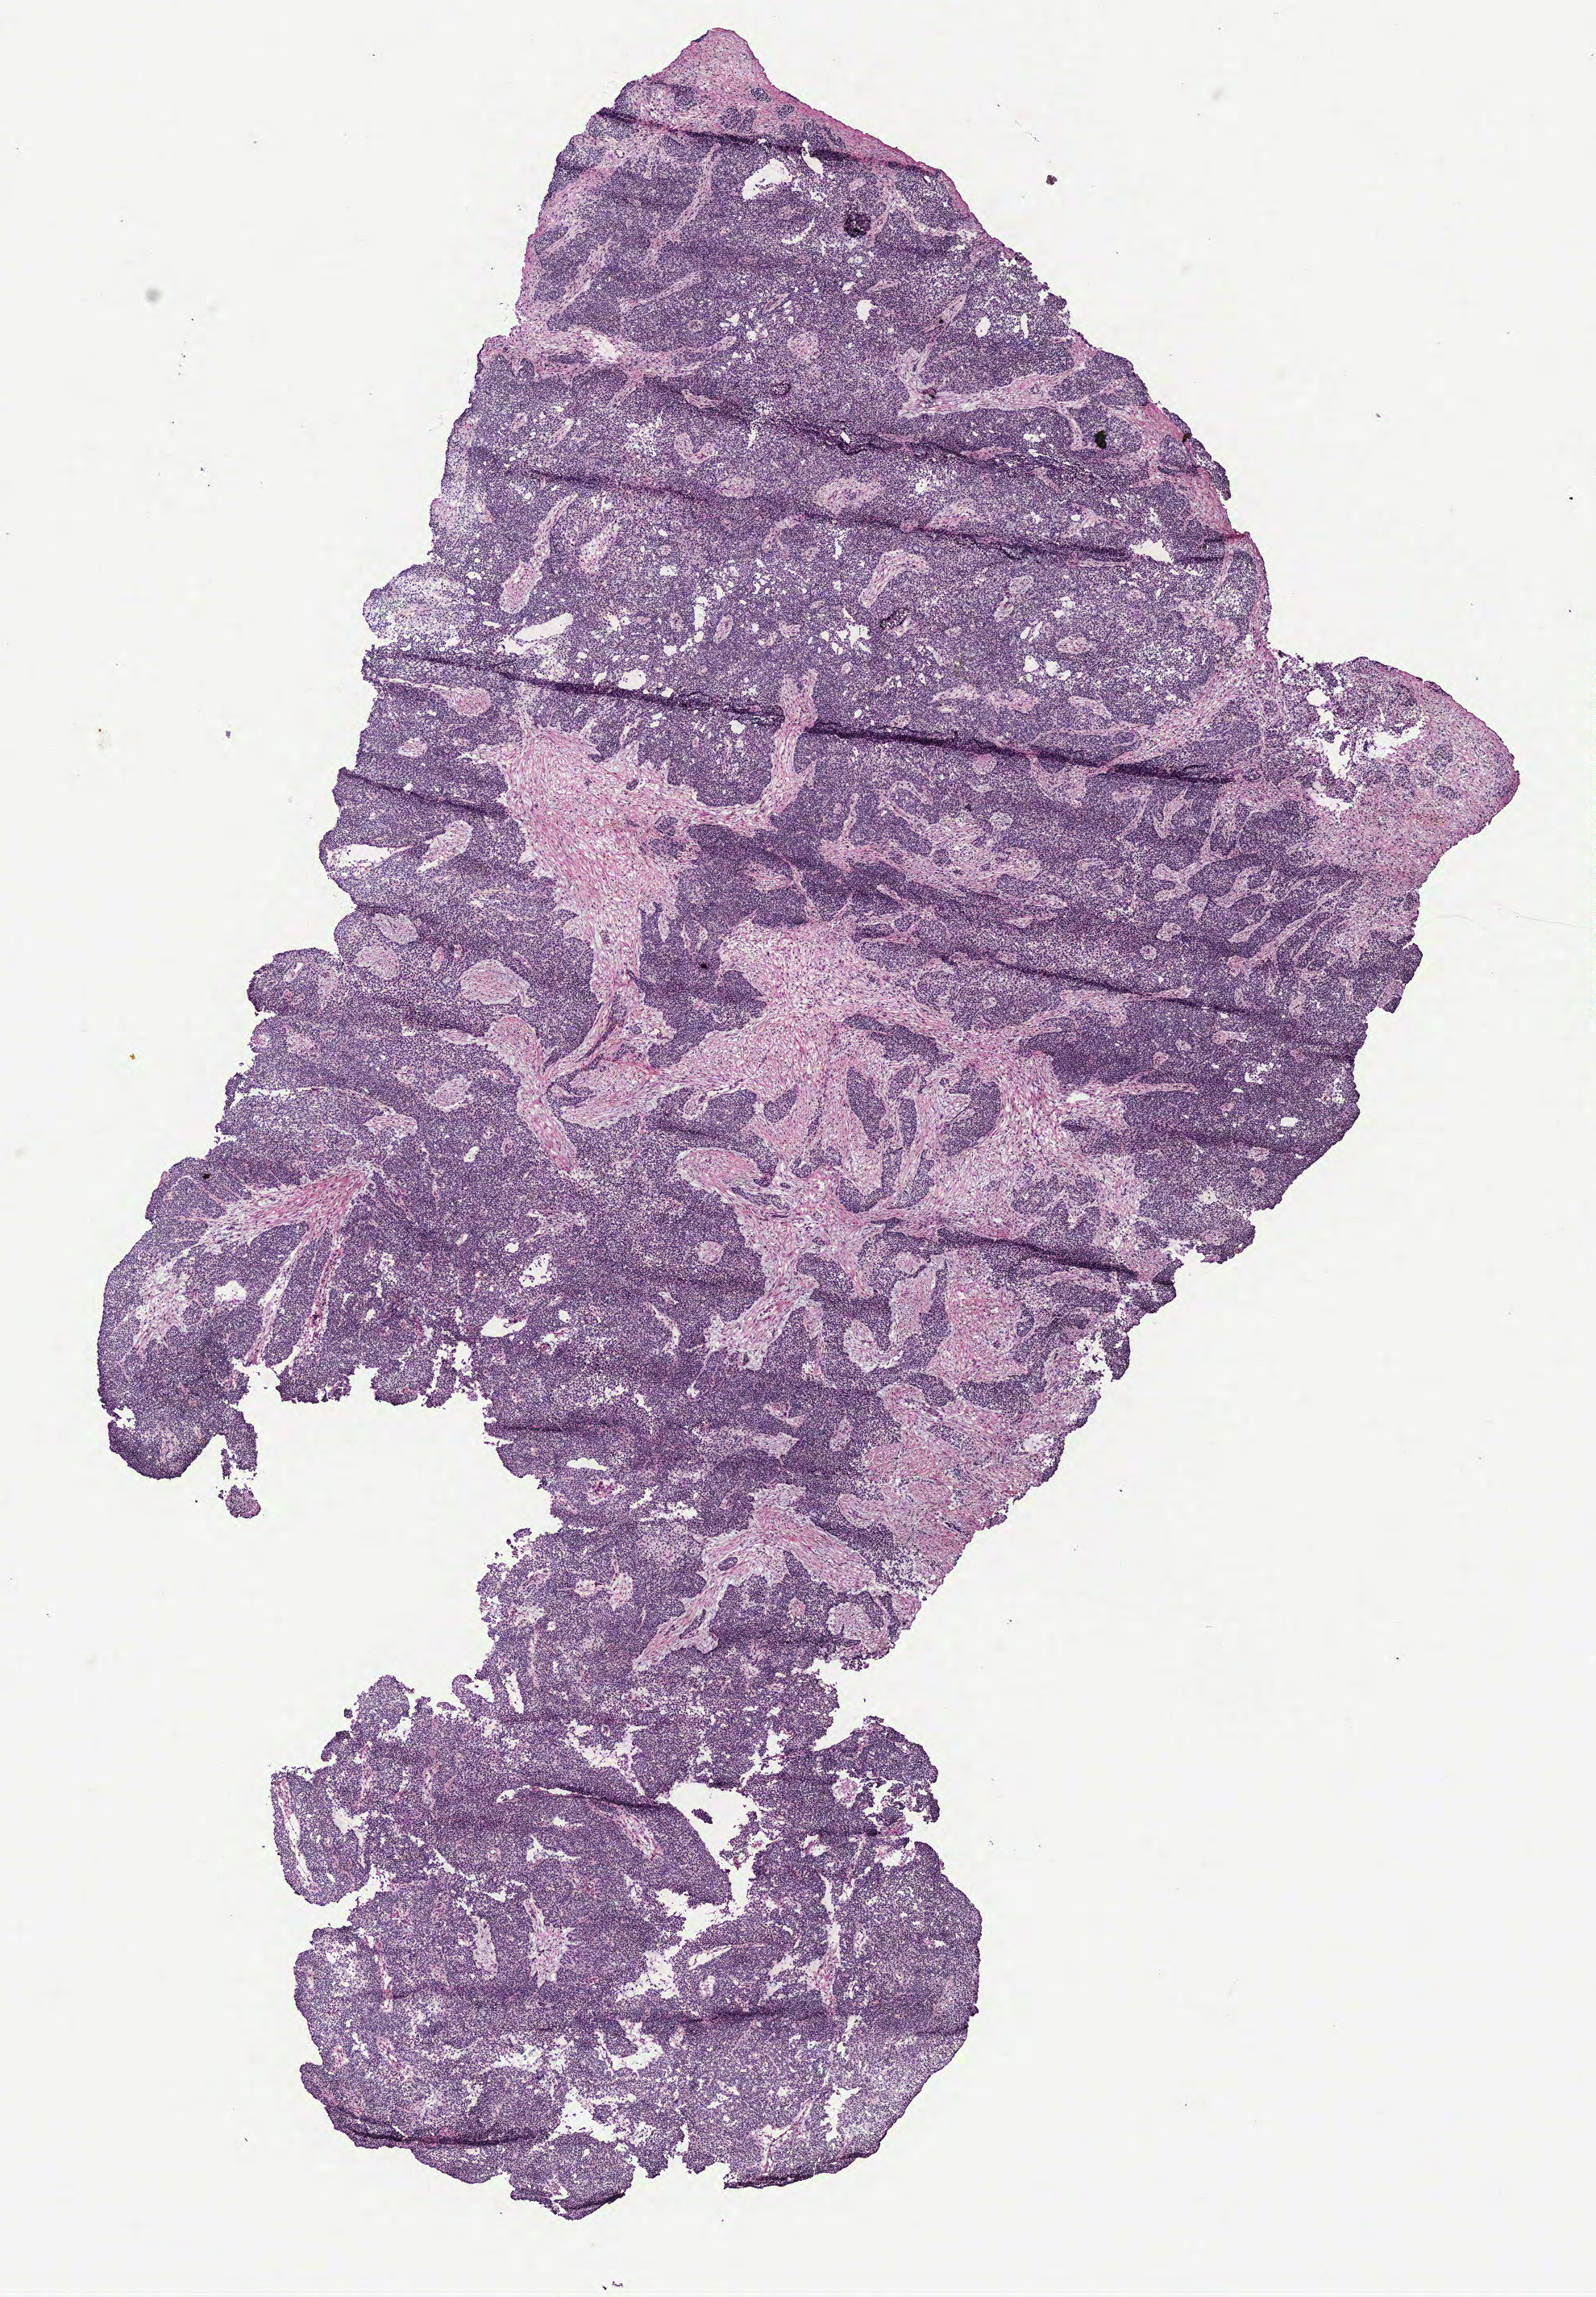
Whole-slide histology image, Hematoxylin and eosin (H&E) stained, whole scanned area (about 7.9 x 11.4 mm) shown as a low-resolution overview. Tumour tissue sample, ovary. 48-year-old female patient.
• primary tumour site (as recorded): ovary
• histologic diagnosis: Serous adenocarcinoma, NOS